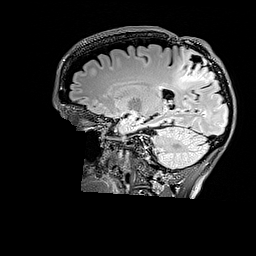
Brain MRI from a brain-tumour surgery series, one sagittal slice. T2 FLAIR. 1 mm slice thickness. 256 × 256 image matrix, field of view 256 × 256 mm. Case-level facts recorded for this patient, not image findings: histopathology: Astrocytoma; WHO grade: 3; IDH mutation: yes.
Structures marked on this image (manually delineated by an expert):
- tumour: bounding box <175,49,216,87> (left, top, right, bottom; pixels)
- tumour: <185,60,214,83>